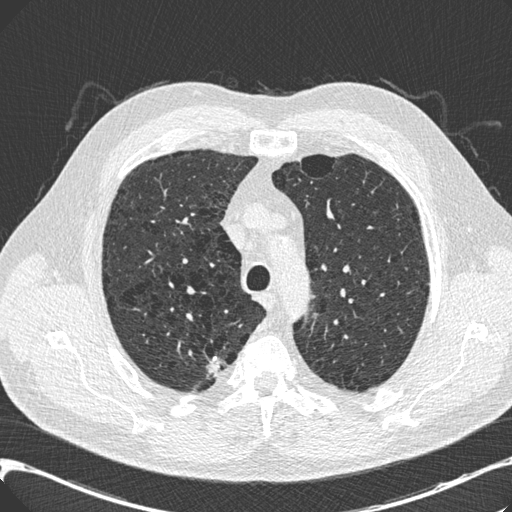
Axial slice from a low-dose chest CT screening exam; third annual screen; lung window (W 1500 / L -600 HU); 0.75 mm slice thickness; standard (soft-tissue) reconstruction kernel (B30f); 120 kVp; slice 47 of 197 in the series; 512 × 512 image matrix. Male participant, aged 68 years at enrolment.
Expert reader's lesion annotation, bounding box <189,348,234,390> (left, top, right, bottom; pixels). The screening reader recorded 3 non-calcified nodules or masses ≥4 mm on this exam; which of them this box marks is not recorded. Official screen result: positive, other. Later outcome: lung cancer diagnosed 46 days after this screen — adenocarcinoma, NOS, right upper lobe, well differentiated (G1), stage IB (AJCC 6th edition), 15 mm at pathology.